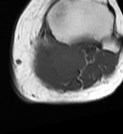
MRI of an extremity soft-tissue mass, one axial slice; position 45 of 68 along the scan axis; MR volume resampled by the dataset authors to the PET/CT grid (not the native acquisition matrix); 123 × 134 image matrix, field of view 120 × 131 mm. Female patient. From the clinical record (not read from this slice): histological type: extraskeletal high grade osteogenic sarcoma; grade: high; site of the primary tumour: left calf.
Annotated regions visible in this slice (expert contour drawn on MRI and transferred to this co-registered scan by the dataset authors):
- gross tumour volume (mass): box from (x=29, y=41) to (x=87, y=85) px